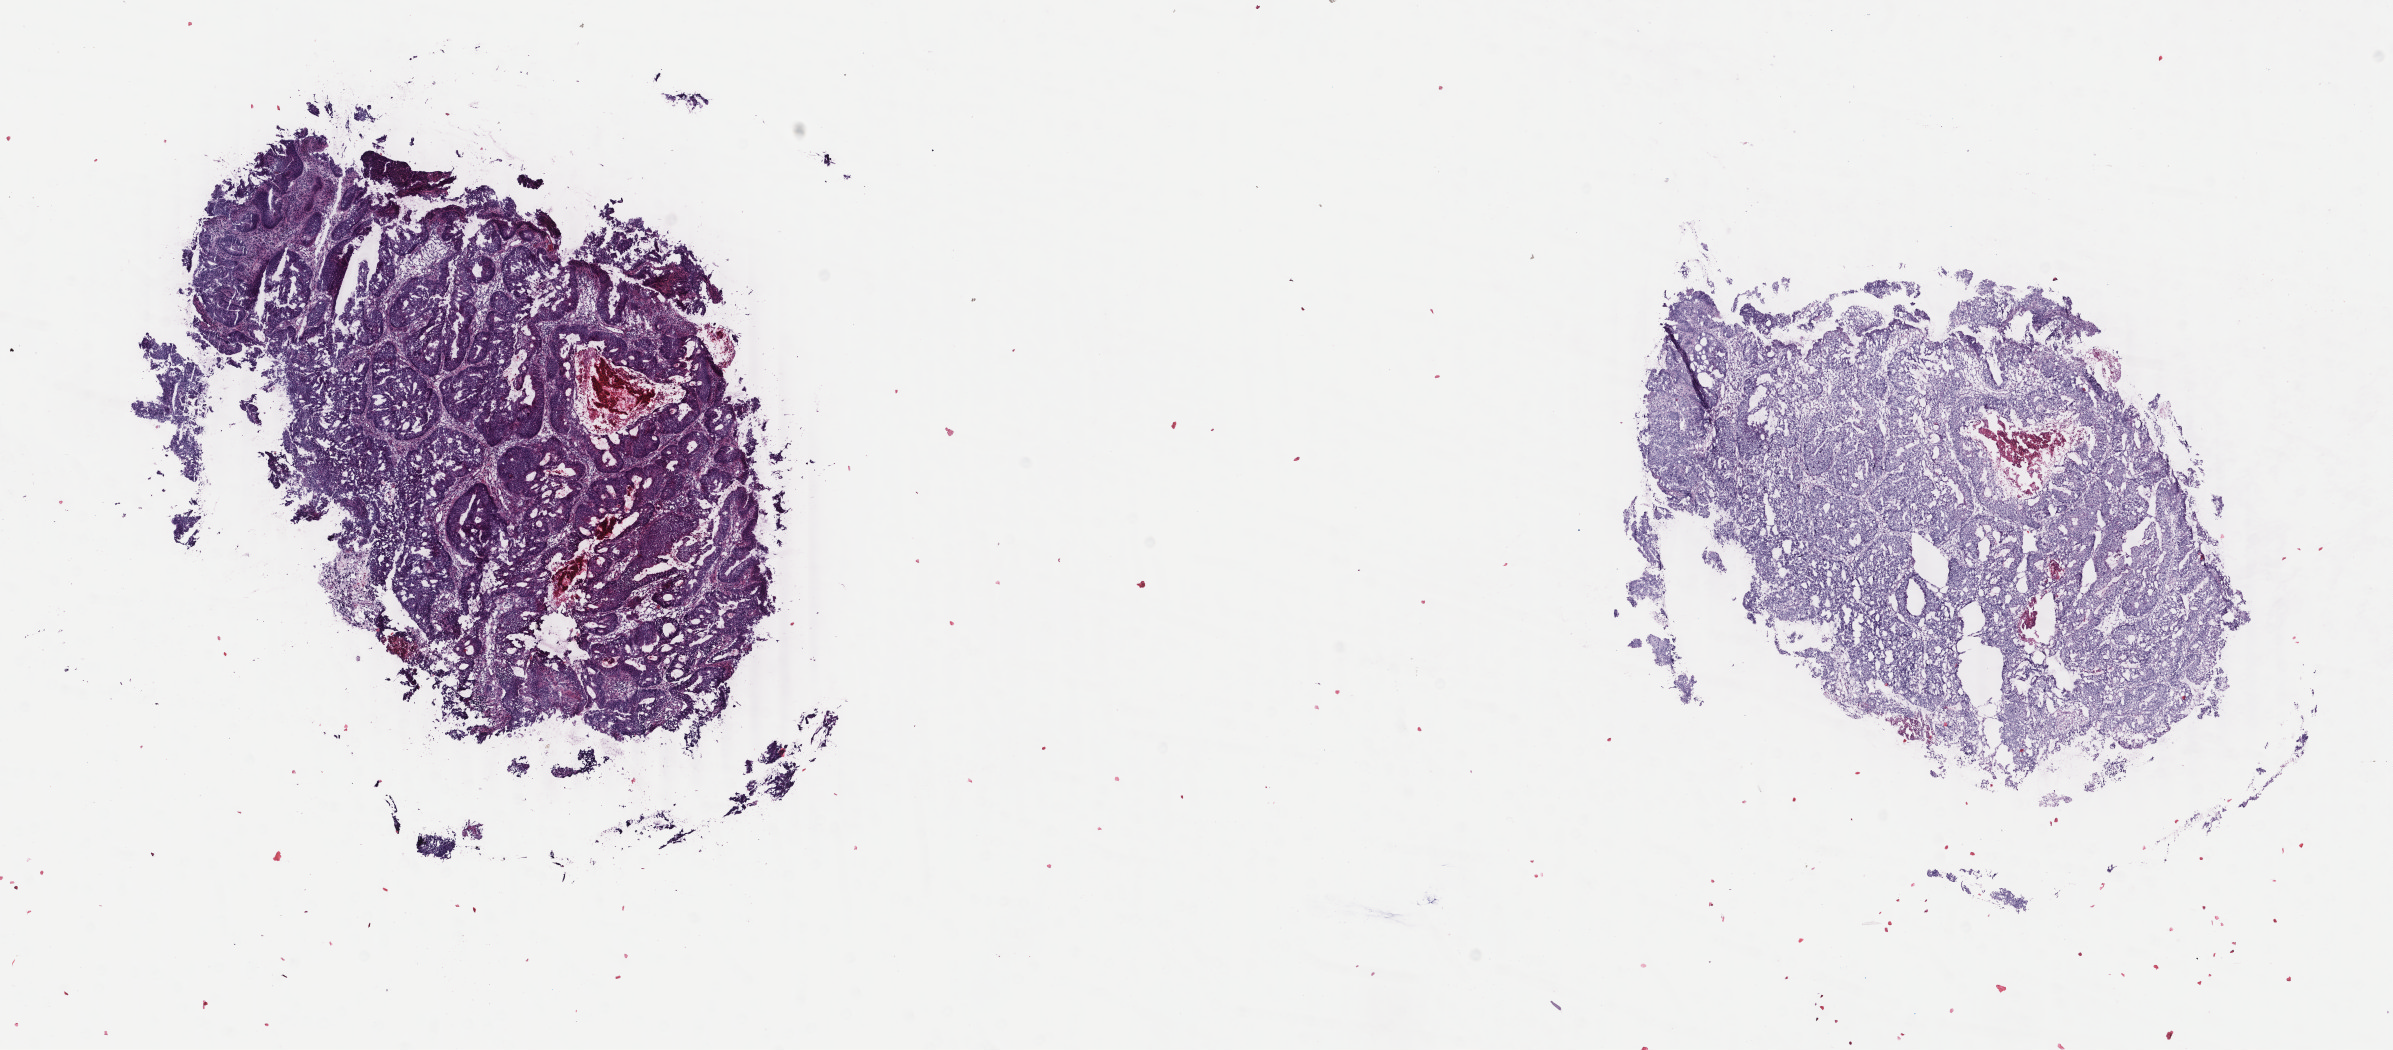
Digitized H&E-stained tissue section (whole slide) — a low-resolution overview of the entire scanned area, about 19.0 x 8.4 mm (slide scanned at 40x); frozen section from the bottom of the tissue portion; primary tumour sample from the colon. Female, age 47 years at initial diagnosis. Slide review estimates, as recorded: tumour cells 95%, tumour nuclei 95%, normal cells 0%, stromal cells 3%, necrosis 2%. Inflammatory infiltration, as recorded: lymphocyte infiltration 1%, monocyte infiltration 0%, neutrophil infiltration 0%.
TNM: T3 N1 M0. Histologic diagnosis: Adenocarcinoma, NOS (sigmoid colon). AJCC pathologic stage: III (5th edition). Lymph nodes positive (case pathology): 1 of 19 examined.